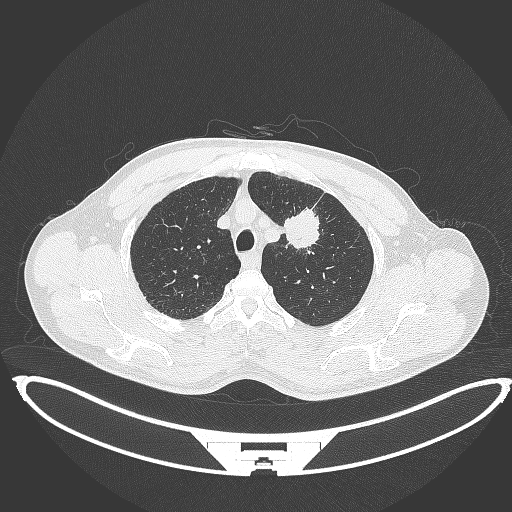
Chest CT, one axial slice. Slice 357 of 395 in the series (ordered by position). Reconstruction kernel B70f. 120 kVp. Lung window (W 1500 / L -600 HU). 512 × 512 image matrix, field of view 457 × 457 mm. Patient: male, 60 years. From the clinical record (not read from this slice): clinical TNM (as recorded): T2a N0 M0; histopathological grade: G1-G2.
Annotated regions visible in this slice (rectangle marked by the reading radiologist):
- lung tumour (recorded histology: squamous cell carcinoma): bounding box [x1, y1, x2, y2] px = [281, 204, 322, 253]